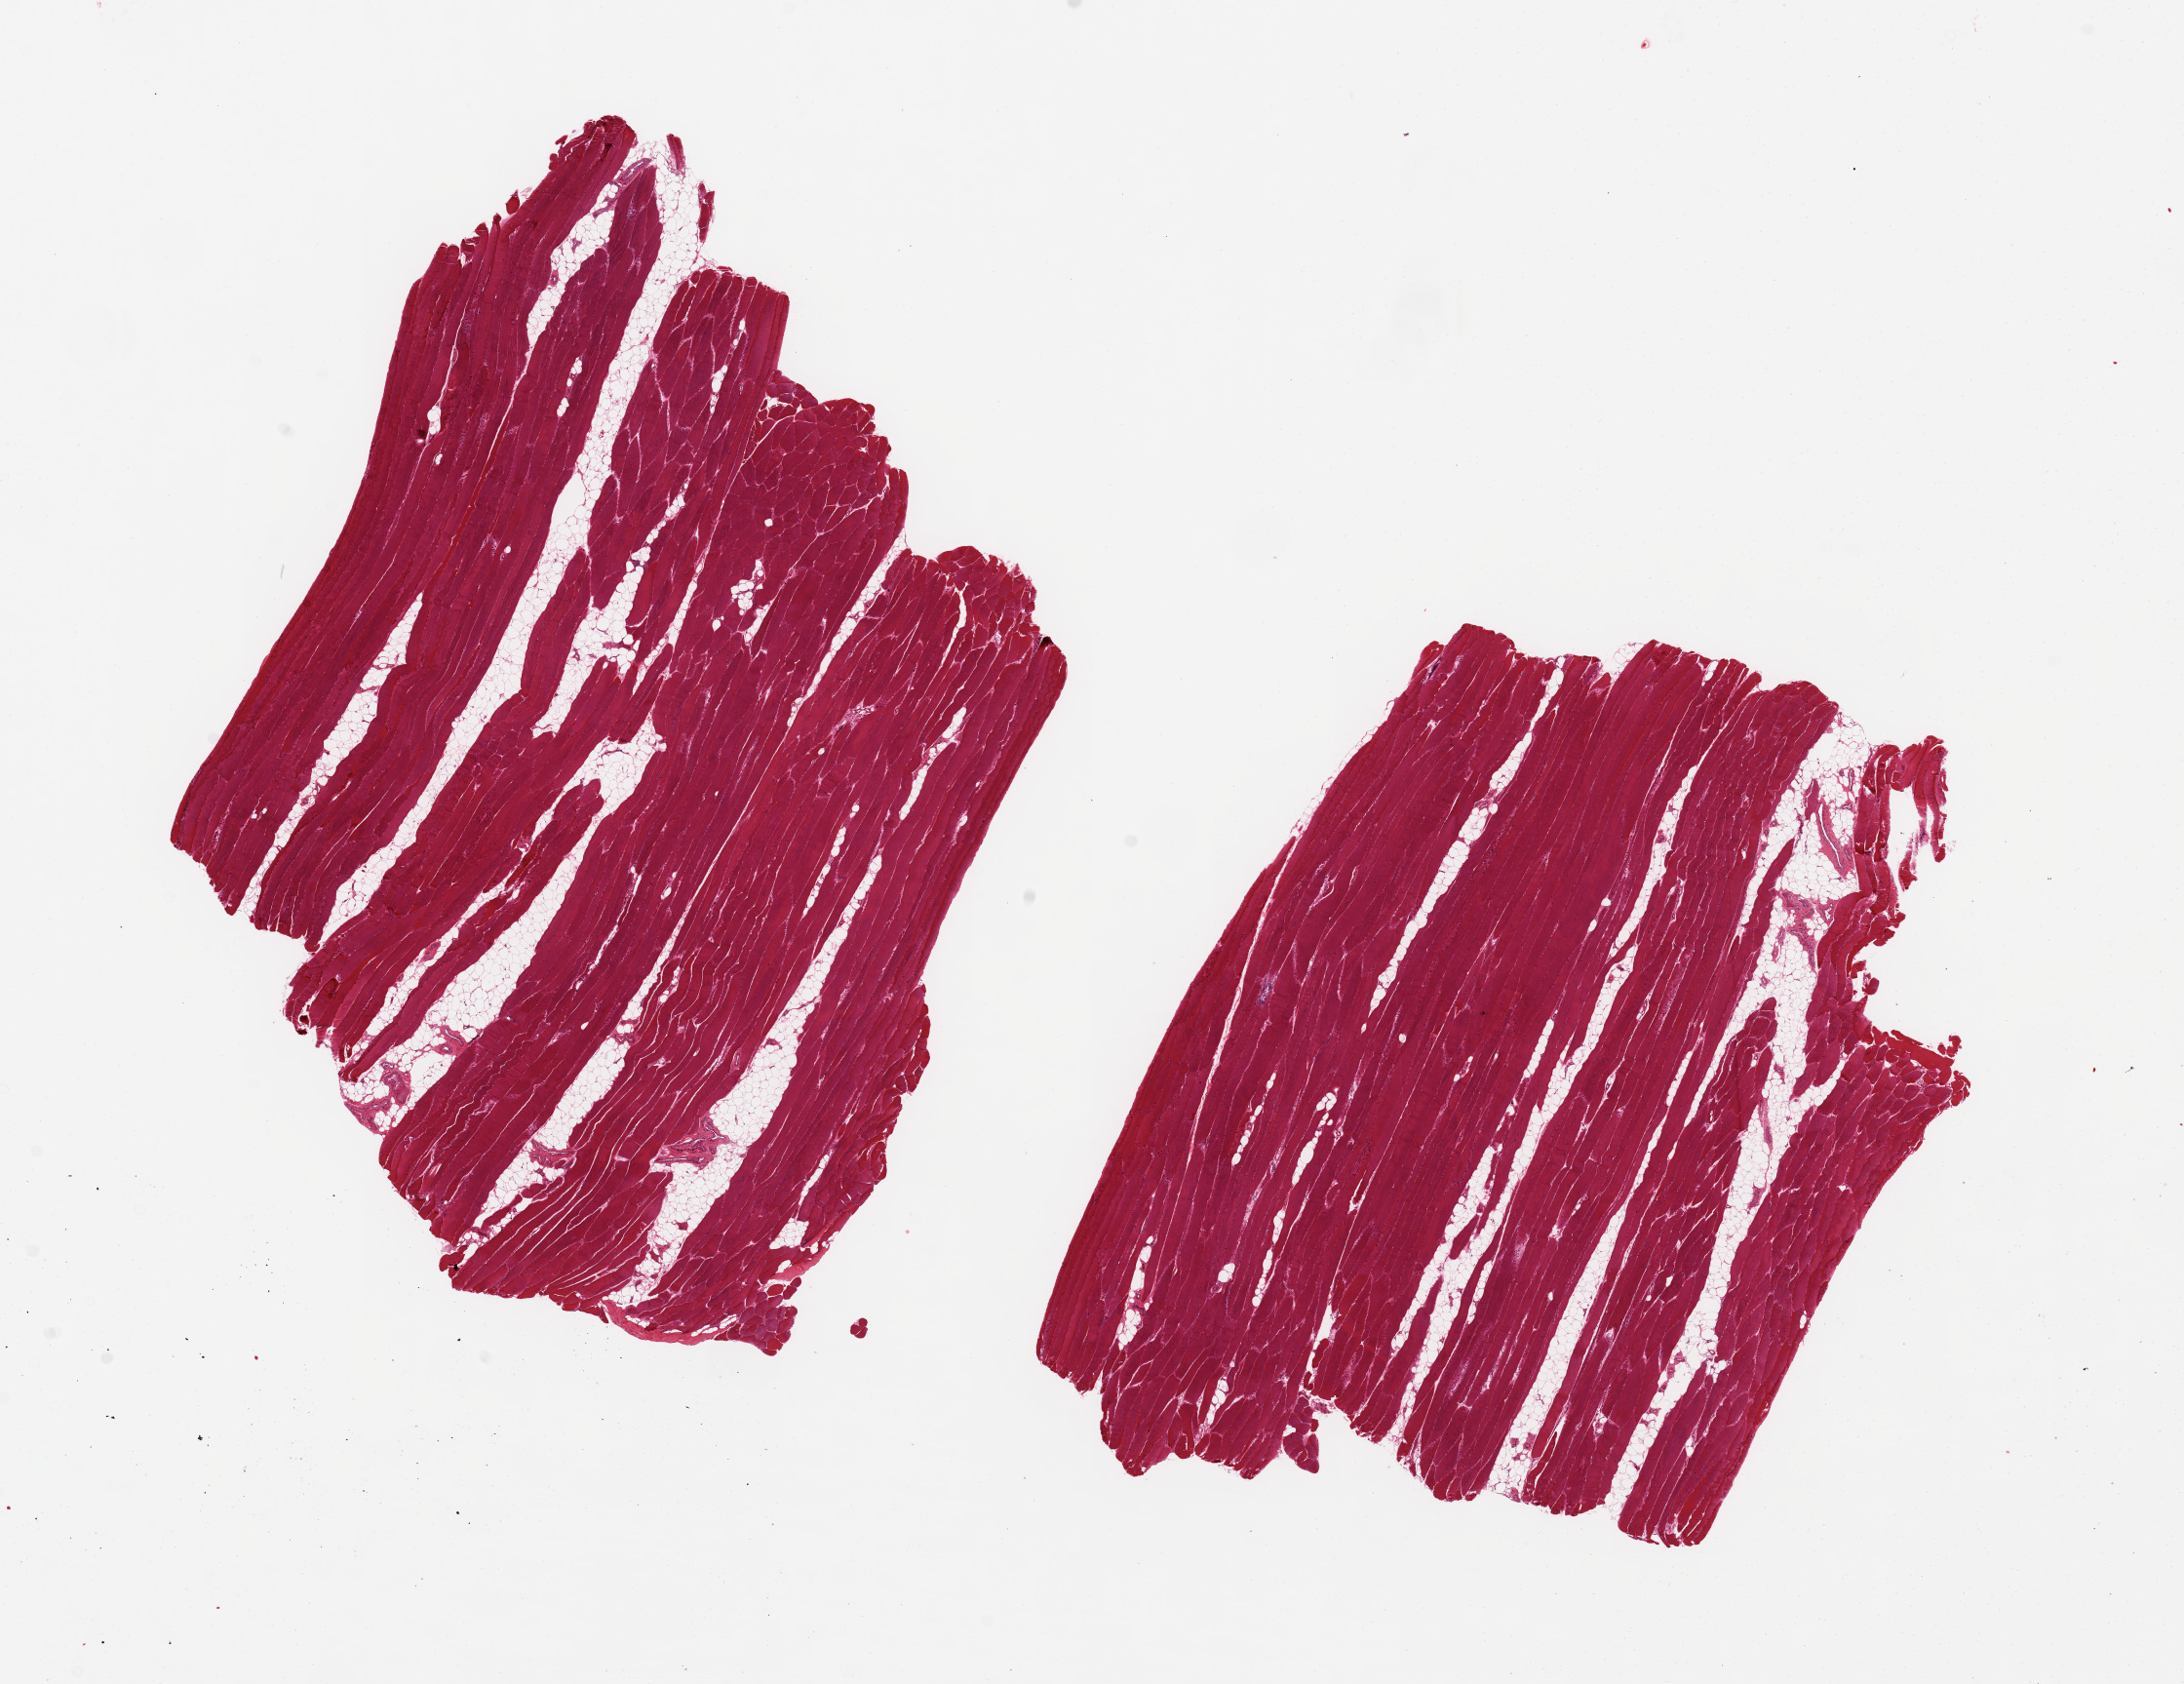
Whole-slide image, haematoxylin and eosin stain, a low-resolution overview of the entire scanned area, about 17.7 x 13.7 mm (from a 20x scan); PAXgene-fixed, paraffin-embedded tissue; section of skeletal muscle (target tissue); donor tissue sample. Donor sex: female.
Reviewer comment on this tissue sample: 2 ~7x6.5mm aliquots, ~20% interspersed fat.